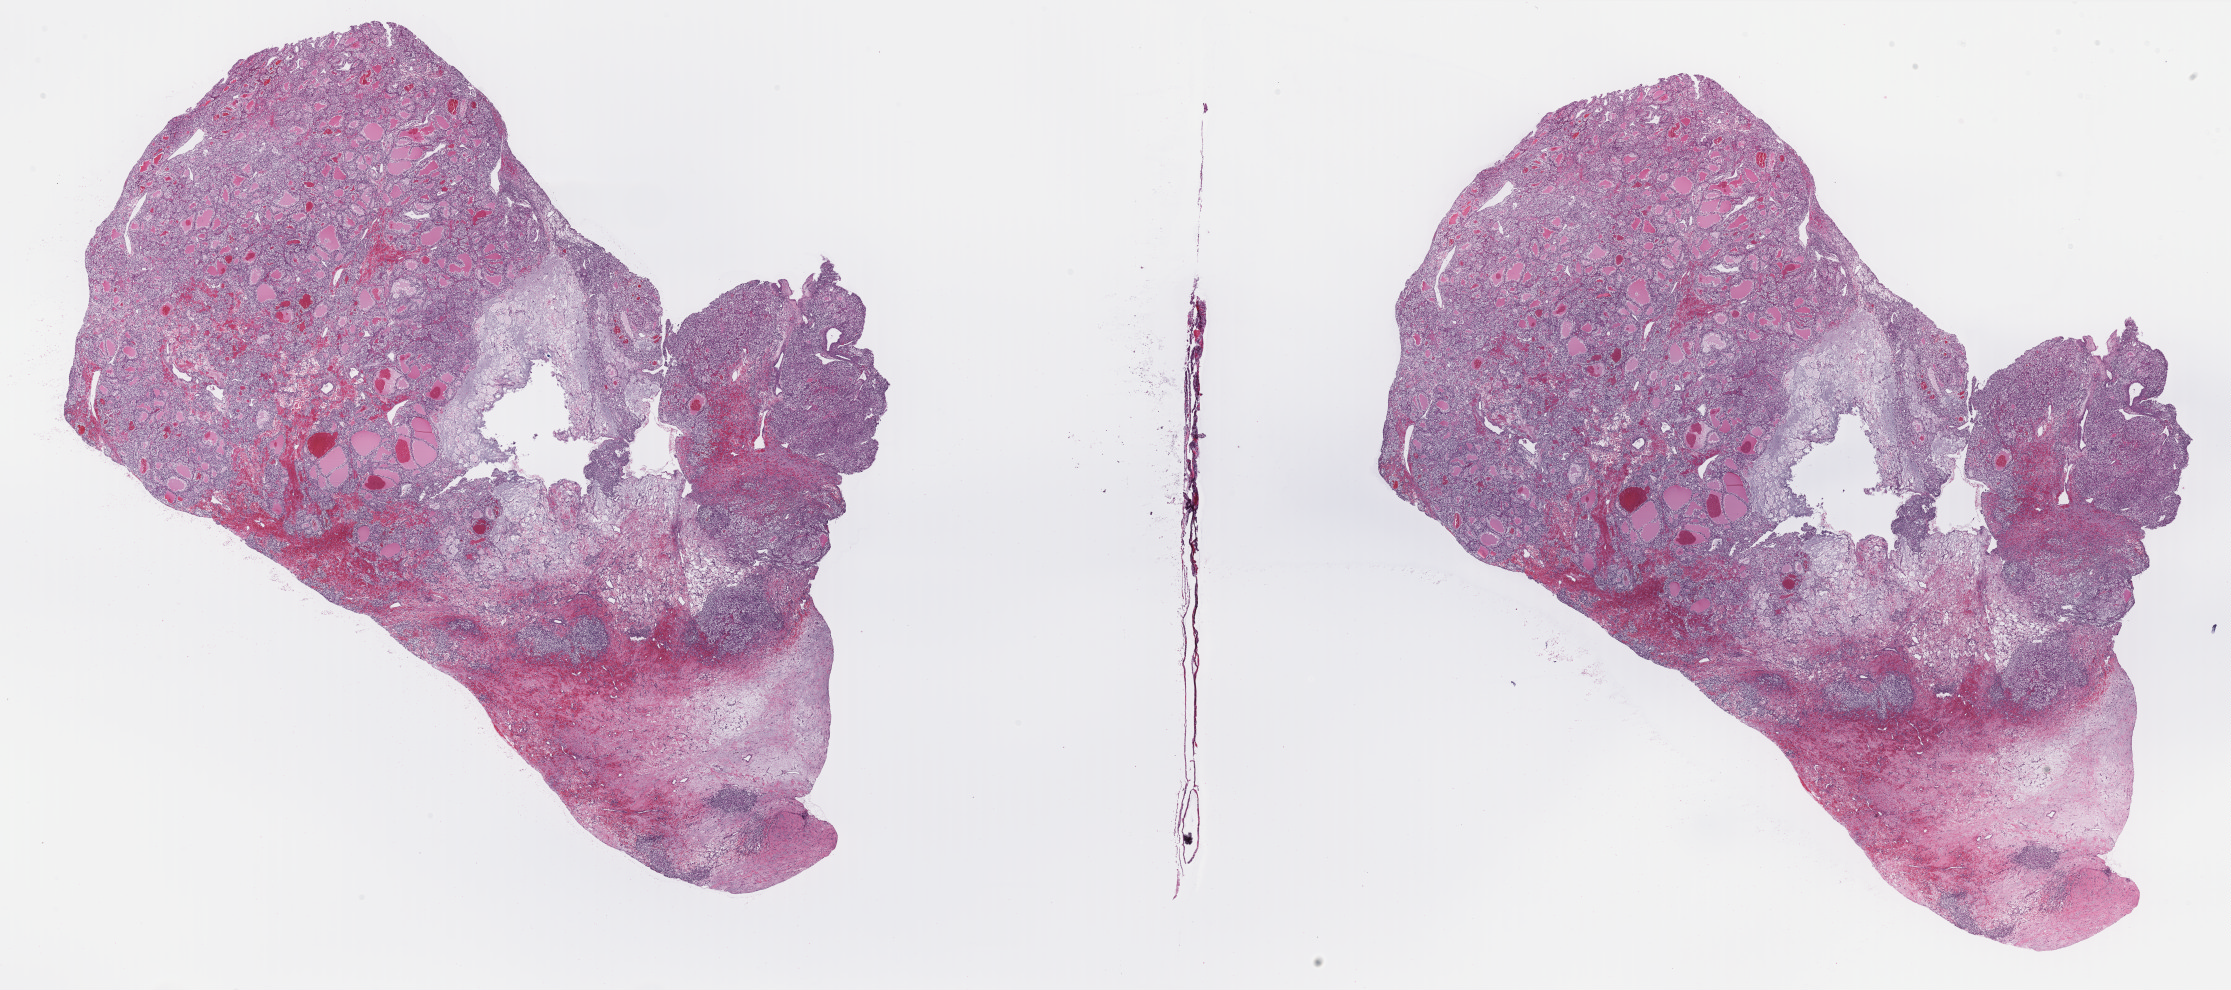
Digitized H&E tissue section (whole slide), a low-resolution overview of the entire scanned area, about 35.3 x 15.7 mm. Formalin-fixed paraffin-embedded (FFPE) diagnostic section. Sample: primary tumour, kidney. Female, age 60 years at initial diagnosis.
Diagnosis: Clear cell adenocarcinoma, NOS.